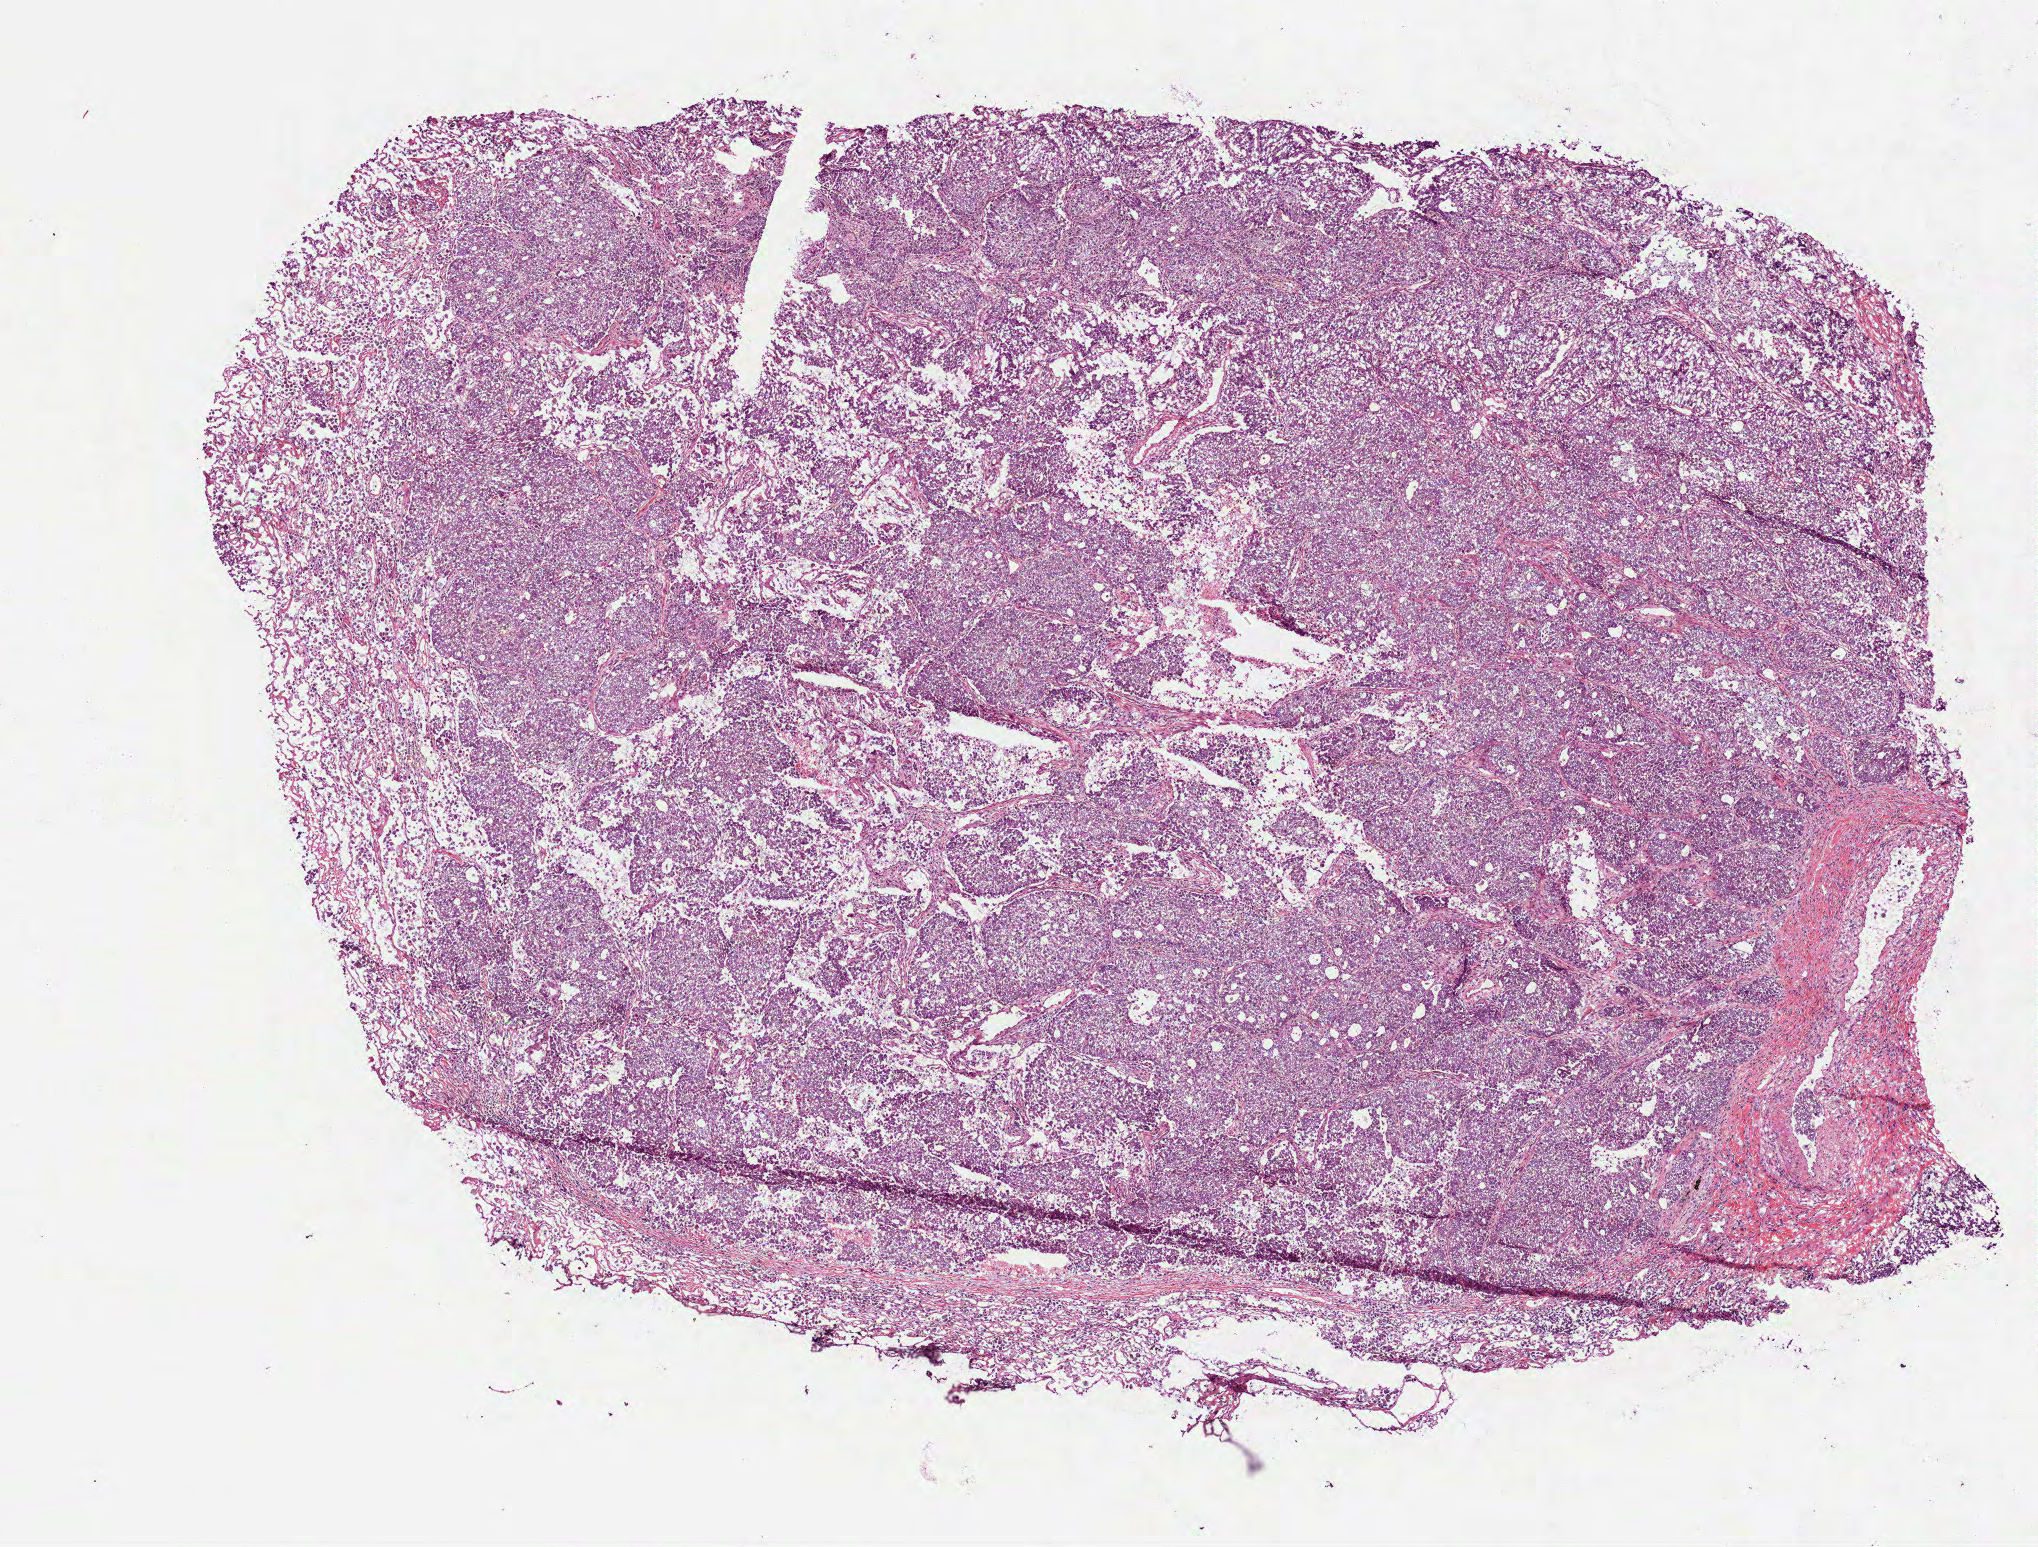
H&E-stained whole-slide image, shown as a low-resolution overview of the whole scanned area (about 8.2 x 6.2 mm, slide scanned at 40x), frozen section, primary tumour sample from the lung. Female, age 53 years at initial diagnosis. Composition of this section per pathologist review: tumour cells 79%, tumour nuclei 80%, normal cells 8%, stromal cells 5%, necrosis 8%.
* pathologic diagnosis: Adenocarcinoma with mixed subtypes (upper lobe, lung)
* AJCC pathologic stage: IIIA (6th edition)